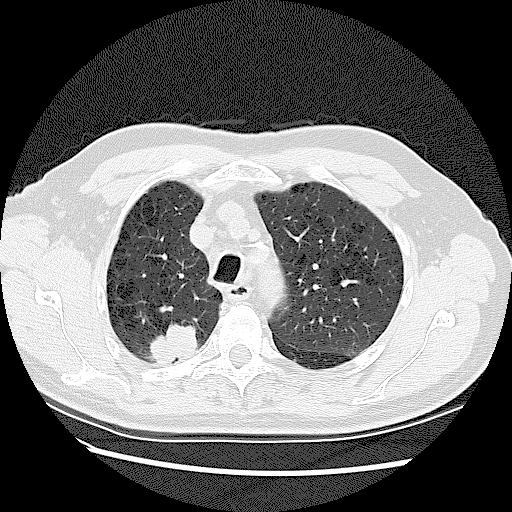
Low-dose screening chest CT, one axial slice; slice 97 of 128 in the series (ordered by position); 120 kVp; lung window (W 1500 / L -600 HU); 2.5 mm slice thickness; 512 × 512 image matrix, field of view 360 × 360 mm.
Structures marked on this image (manually delineated by an expert):
- lesion 2 (tumor, upper lobe of right lung): bounding box <150,323,197,364> (left, top, right, bottom; pixels)